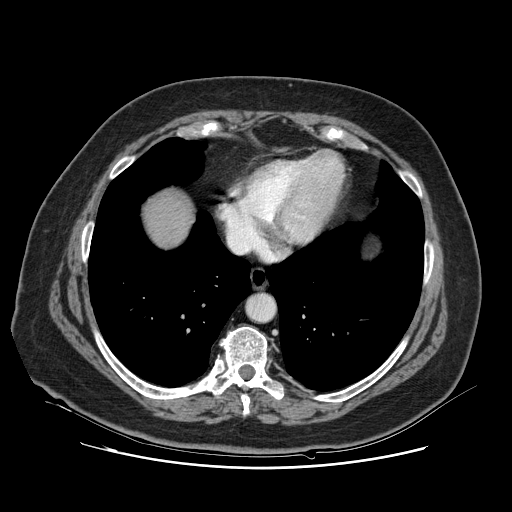
Contrast-enhanced abdominal CT, one axial slice; position 120 of 132 along the scan axis; soft-tissue window (W 400 / L 40 HU); 2.5 mm slice thickness; 512 × 512 image matrix, field of view 391 × 391 mm. Female patient, age 73 years. From the clinical record (not read from this slice): diagnosis: colorectal cancer liver metastases, imaged before liver resection; multiple liver metastases: no; largest metastasis: 7 cm; disease in both lobes: no.
Outlined on this slice (expert manual segmentation):
- liver: bounding box <145,194,191,246> (left, top, right, bottom; pixels)
- planned liver remnant (the part of the liver to remain after resection): <145,194,191,246>